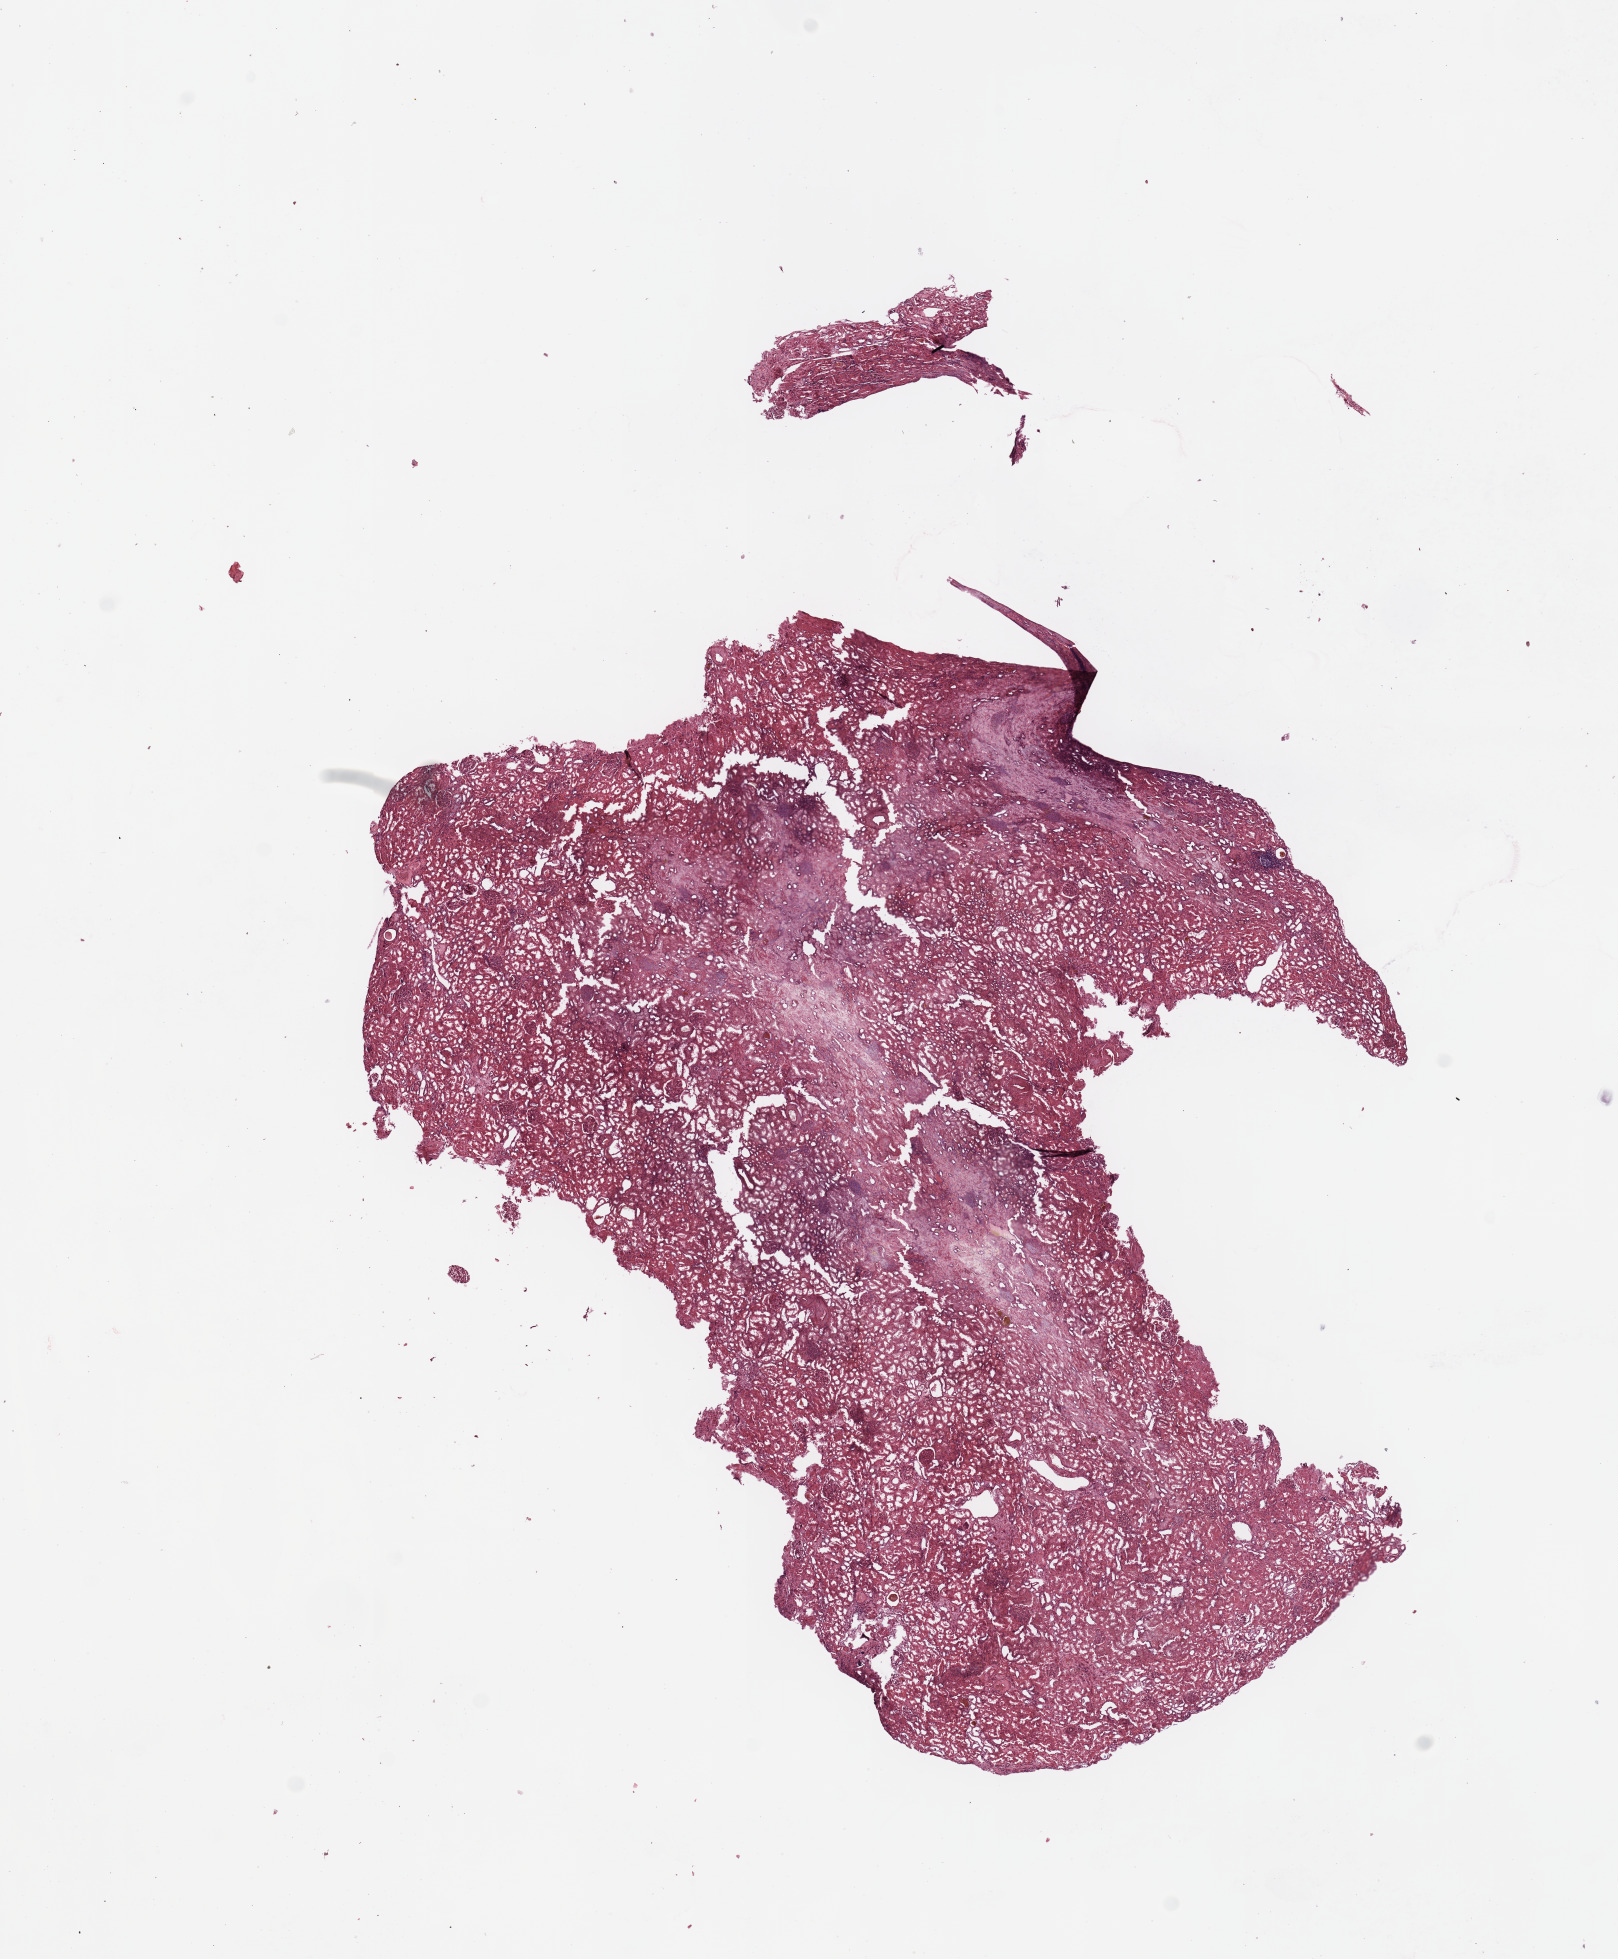
H&E whole-slide image, whole scanned area (about 12.8 x 15.5 mm, acquisition: 20x scan) shown as a low-resolution overview; normal (non-tumour) tissue sample, sampled site: kidney. Female, 67 y/o.
• this section: normal (non-tumour) tissue from the same patient
• patient diagnosis: Renal cell carcinoma, NOS